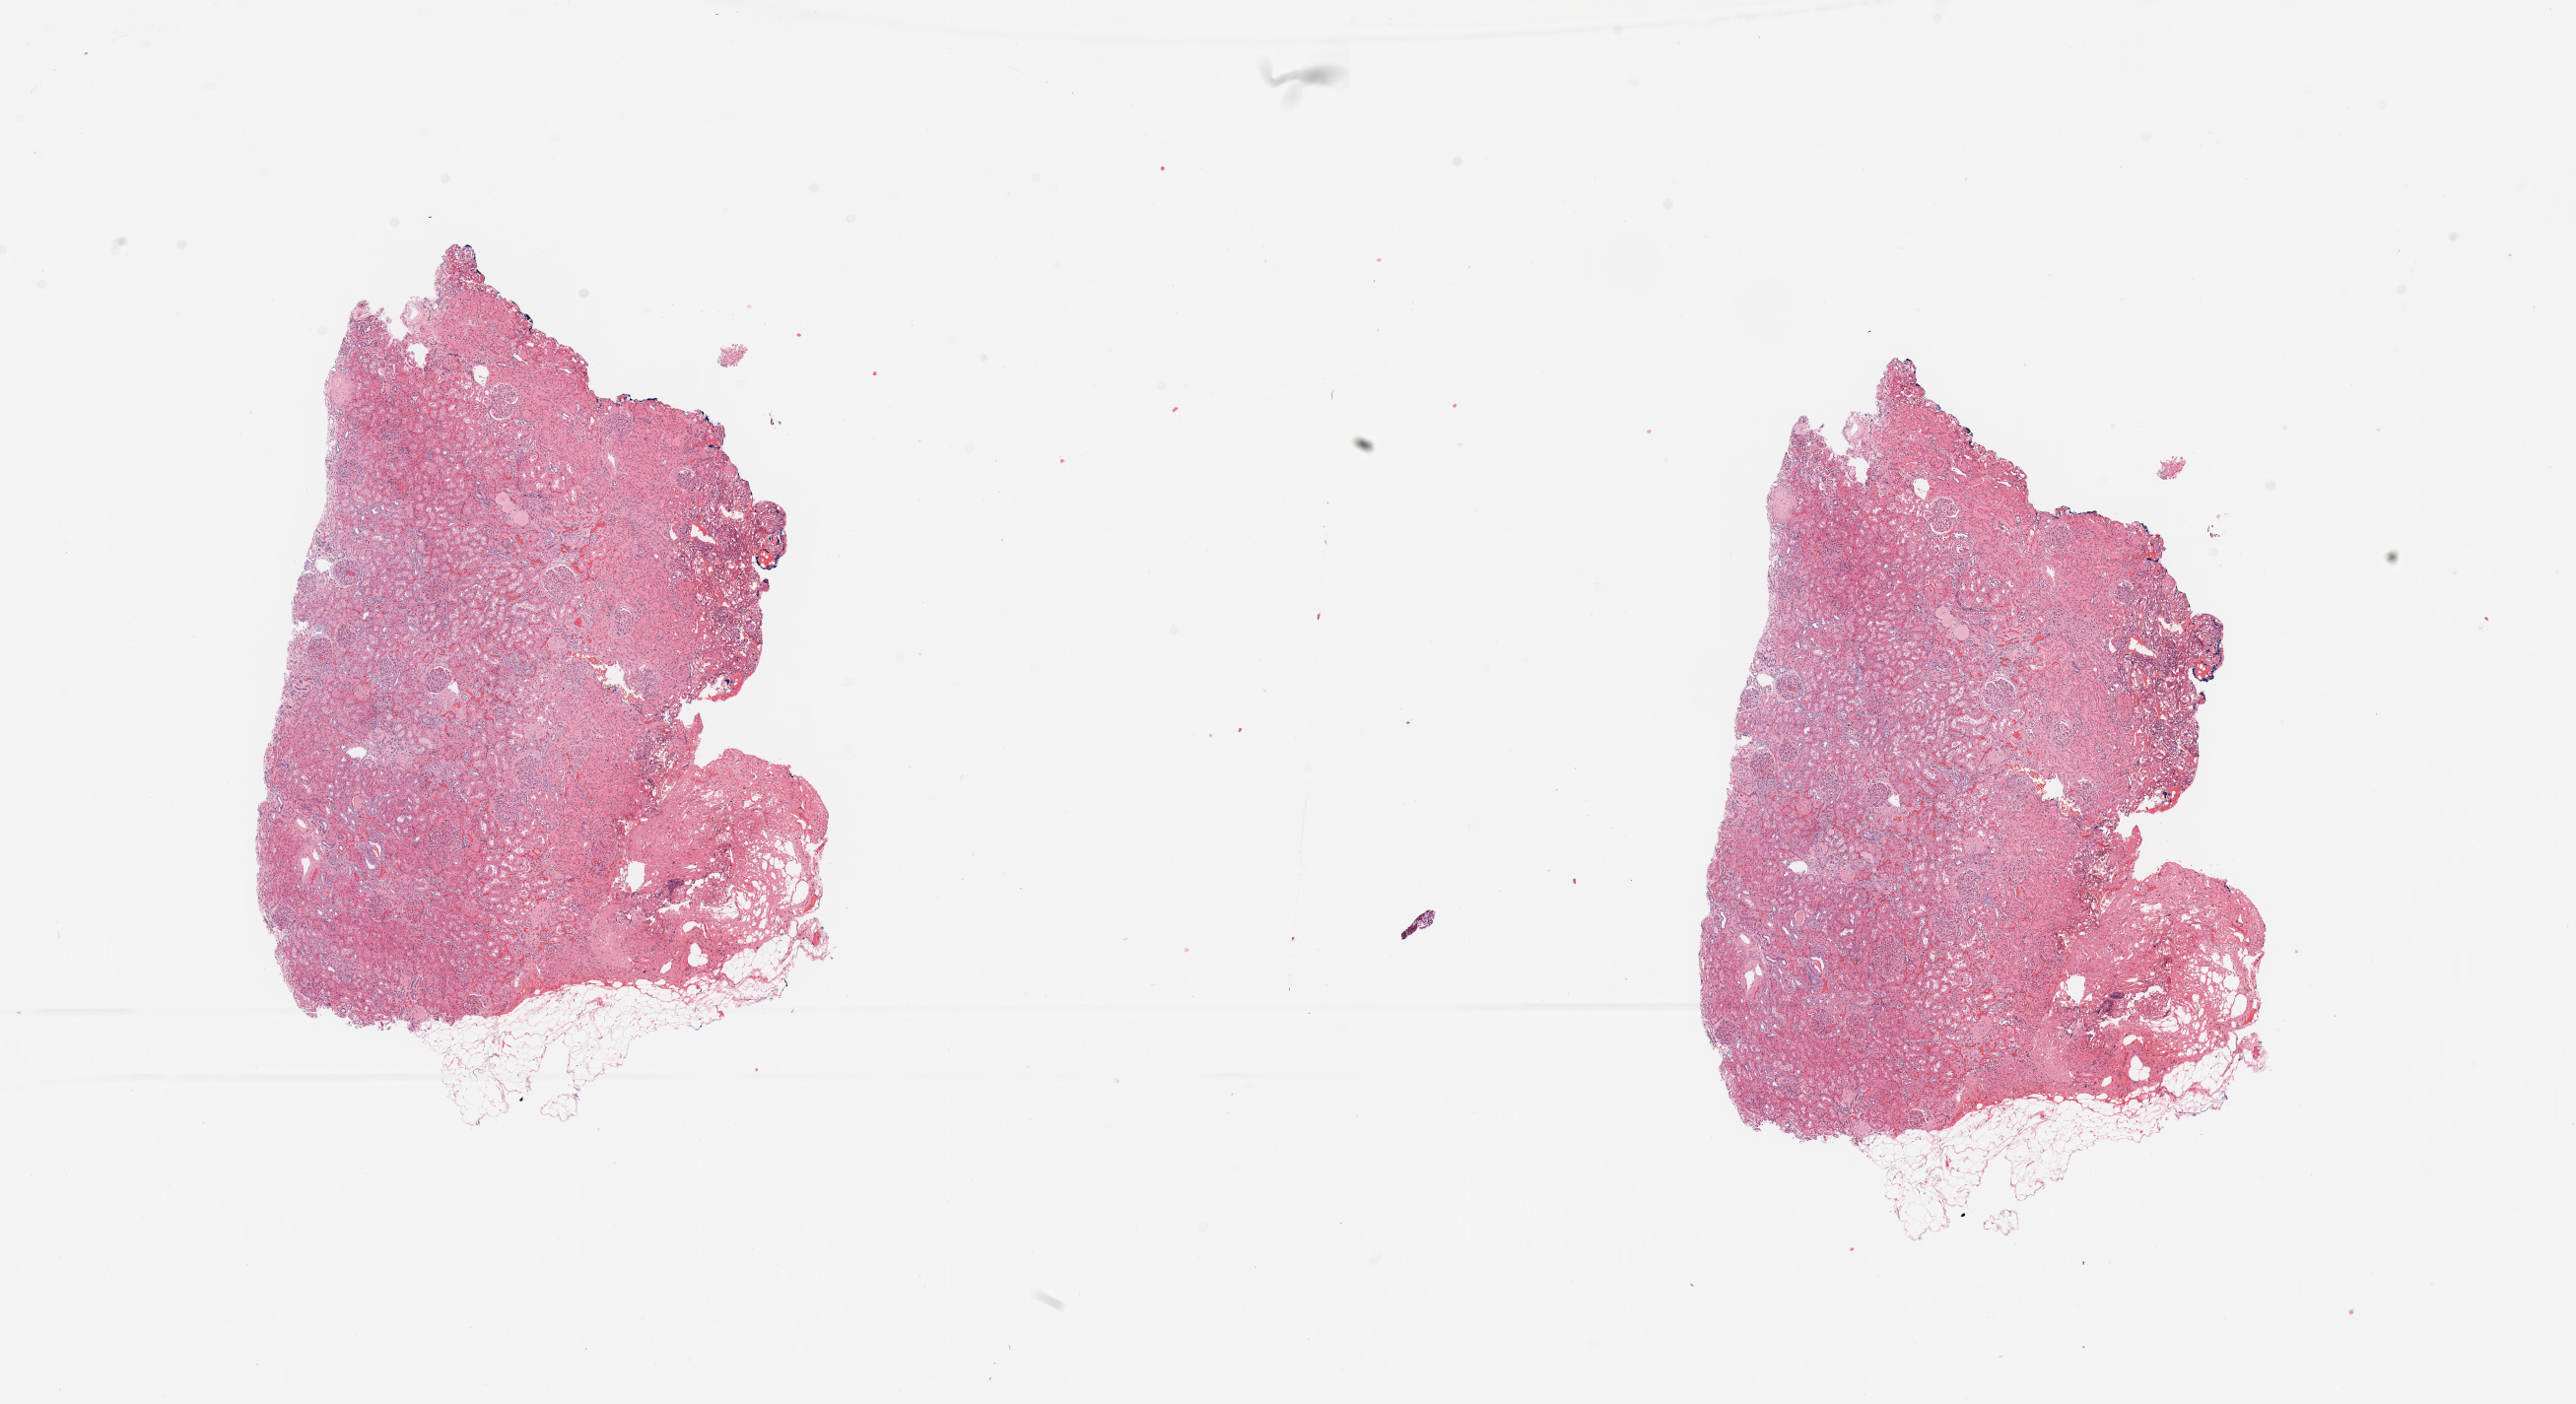
Whole-slide histology image, H&E-stained — a low-resolution overview of the entire scanned area, about 20.7 x 11.3 mm (acquisition: 20x scan); normal (non-tumour) tissue sample, sampled site: kidney. 70-year-old female patient.
This section: normal (non-tumour) tissue from the same patient. Patient diagnosis: Renal cell carcinoma, NOS.